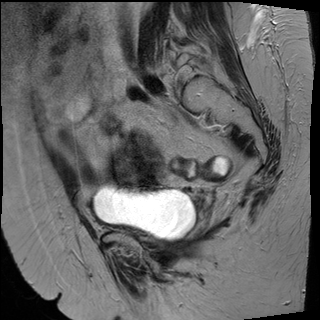
Pelvic MRI for cervical cancer, one sagittal slice; slice 31 of 50 in the series (ordered by position); T2-weighted; 1.5 T; TE 89 ms, TR 4880 ms; 4 mm slice thickness; 320 × 320 image matrix, field of view 260 × 260 mm. Patient: female, 50 years.
Outlined on this slice (manually delineated by an expert):
- uterus and cervix: bounding box [x1, y1, x2, y2] px = [109, 129, 167, 192]